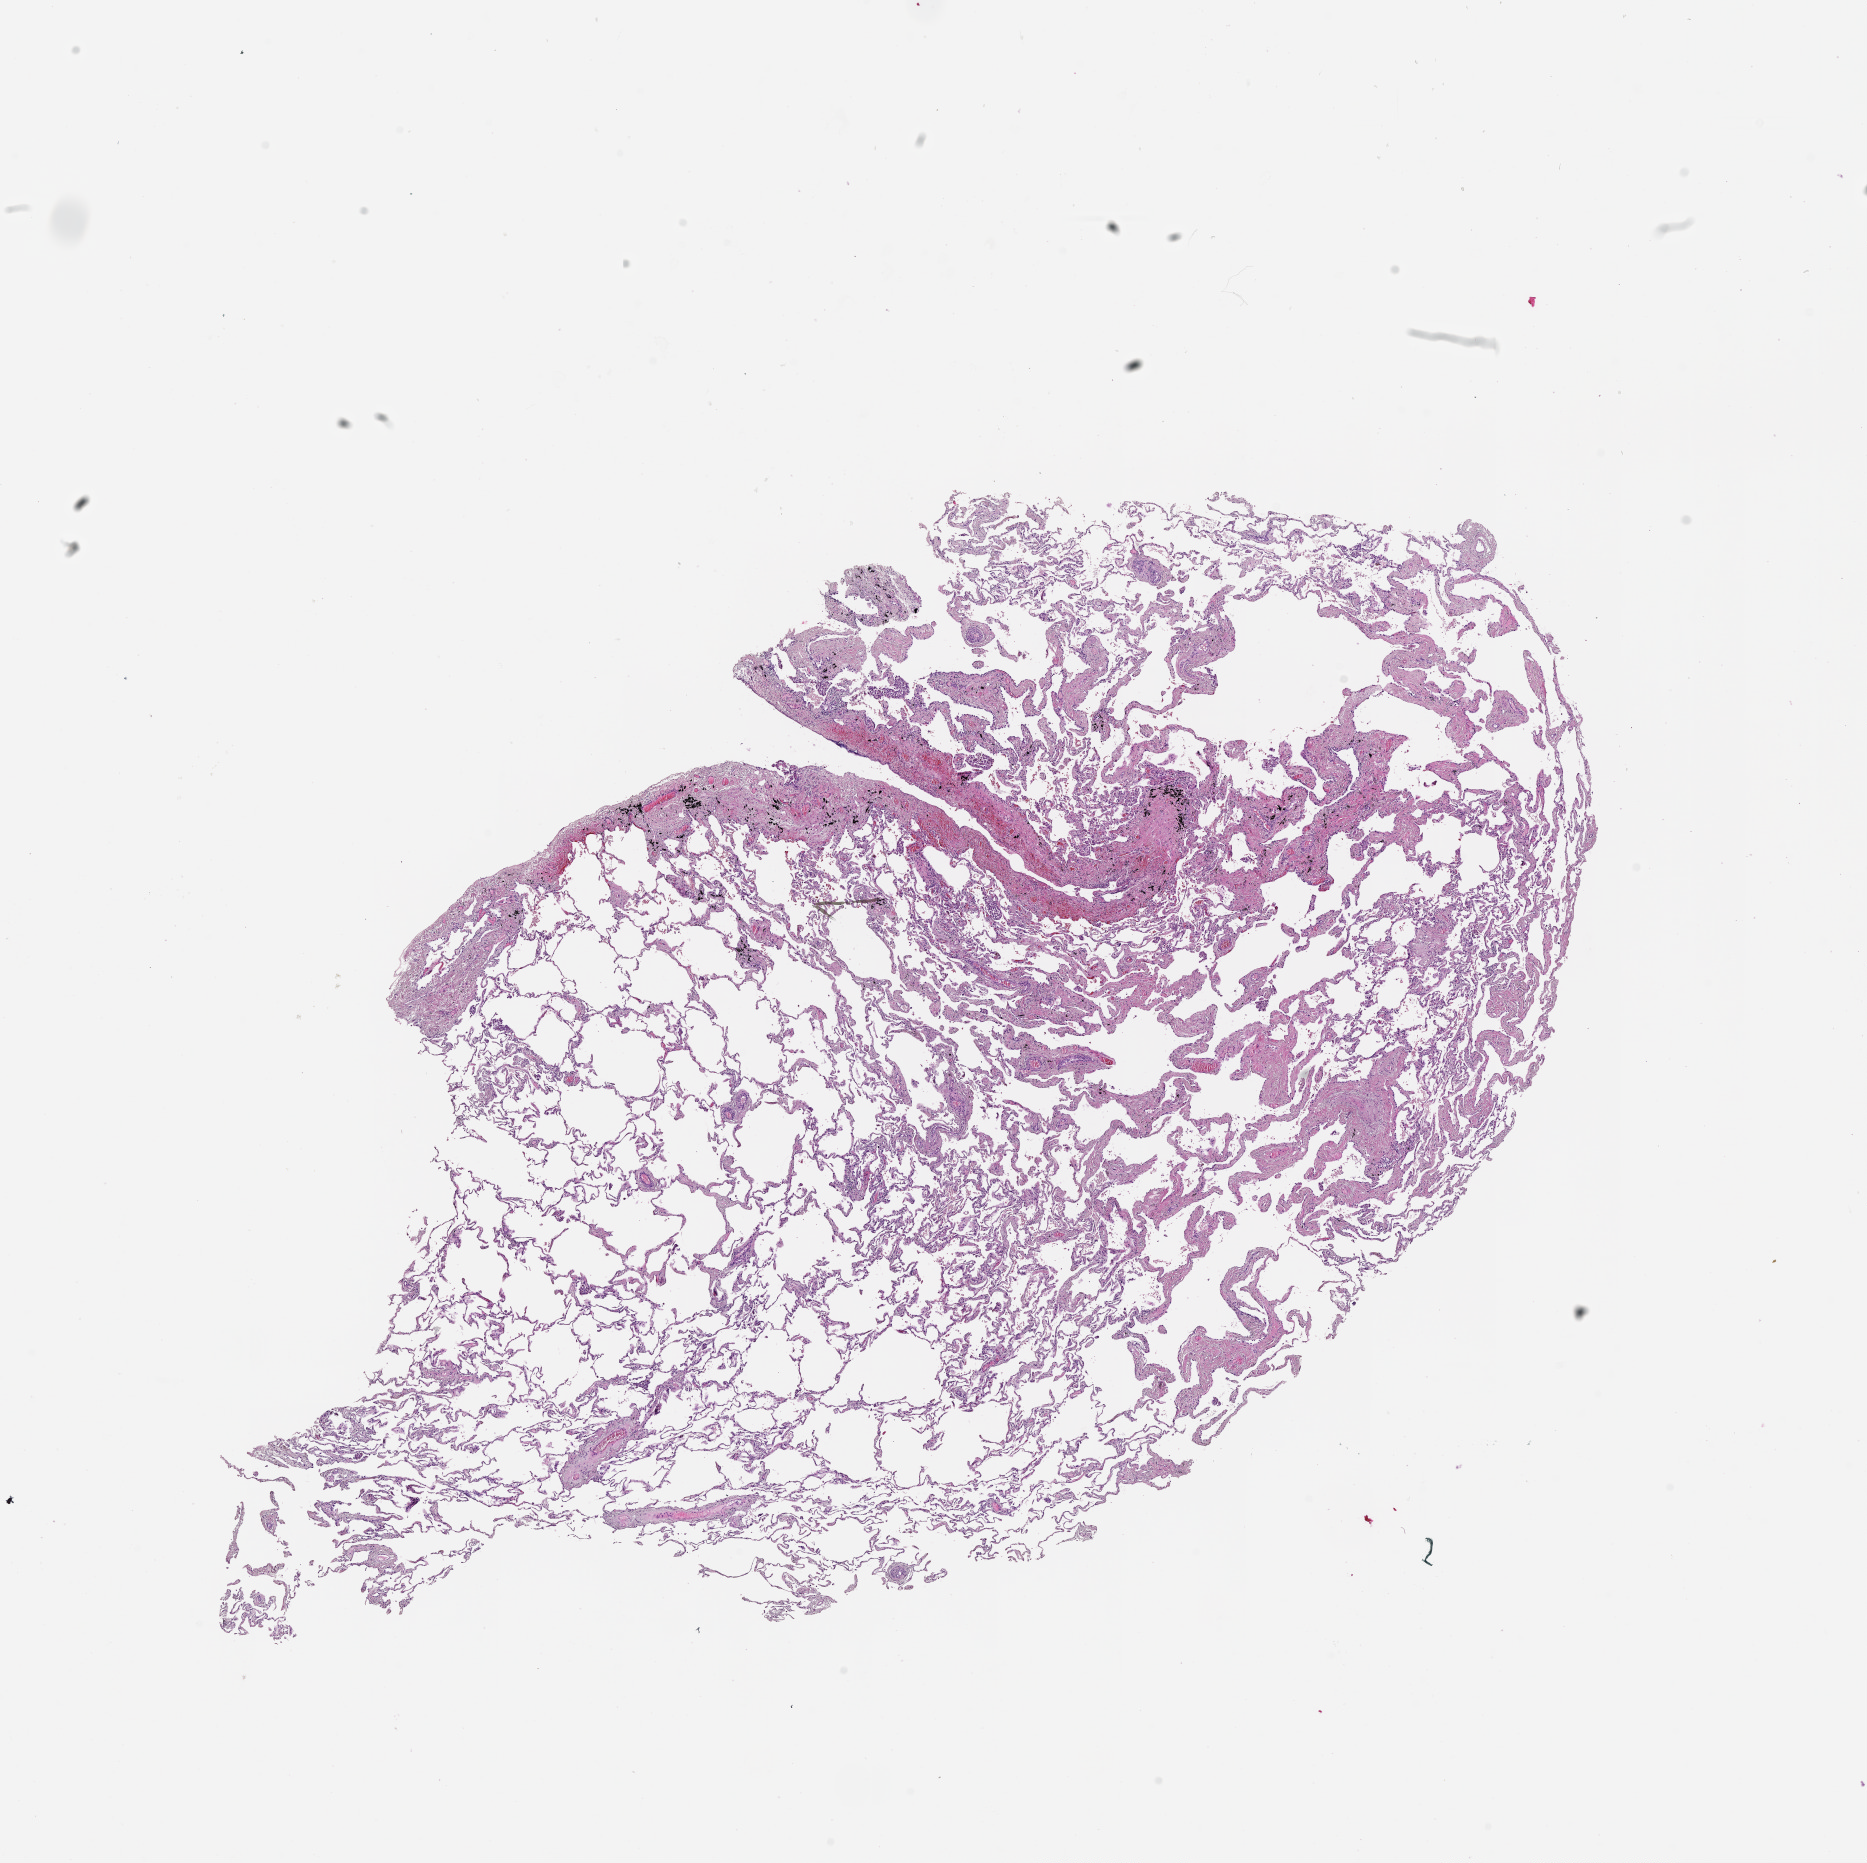
Whole-slide histology image, H&E-stained — shown as a low-resolution overview of the whole scanned area (about 15.0 x 15.0 mm, slide scanned at 20x); normal (non-tumour) tissue sample, lung. 77-year-old male patient.
This section: normal (non-tumour) tissue from the same patient. Patient diagnosis (cohort enrolment): squamous cell carcinoma (lung).